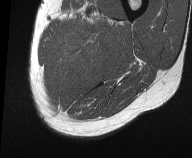
MRI of an extremity soft-tissue mass, one axial slice. MR volume resampled by the dataset authors to the PET/CT grid (not the native acquisition matrix). 3.27 mm slice thickness. 192 × 158 image matrix, field of view 187 × 154 mm. Male patient. Case-level facts recorded for this patient, not image findings: histological type: pleiomorphic liposarcoma; grade: high; site of the primary tumour: left thigh.
Annotated regions visible in this slice (expert contour drawn on MRI and transferred to this co-registered scan by the dataset authors):
- gross tumour volume including surrounding oedema: bounding box <66,14,115,63> (left, top, right, bottom; pixels)